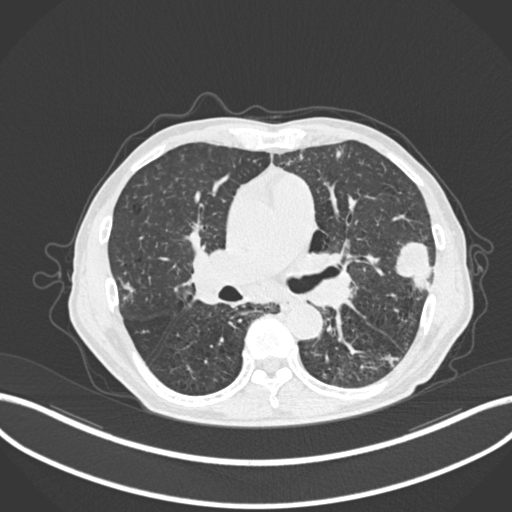
Chest CT, one axial slice; position 133 of 287 along the scan axis; reconstruction kernel B30f; lung window (W 1500 / L -600 HU); 1 mm slice thickness; 512 × 512 image matrix, field of view 400 × 400 mm. Patient: male, 74 years. From the clinical record (not read from this slice): clinical TNM (as recorded): T2a N1 M0.
Outlined on this slice (bounding box drawn by a radiologist):
- lung tumour (recorded histology: adenocarcinoma): bounding box <396,236,433,293> (left, top, right, bottom; pixels)